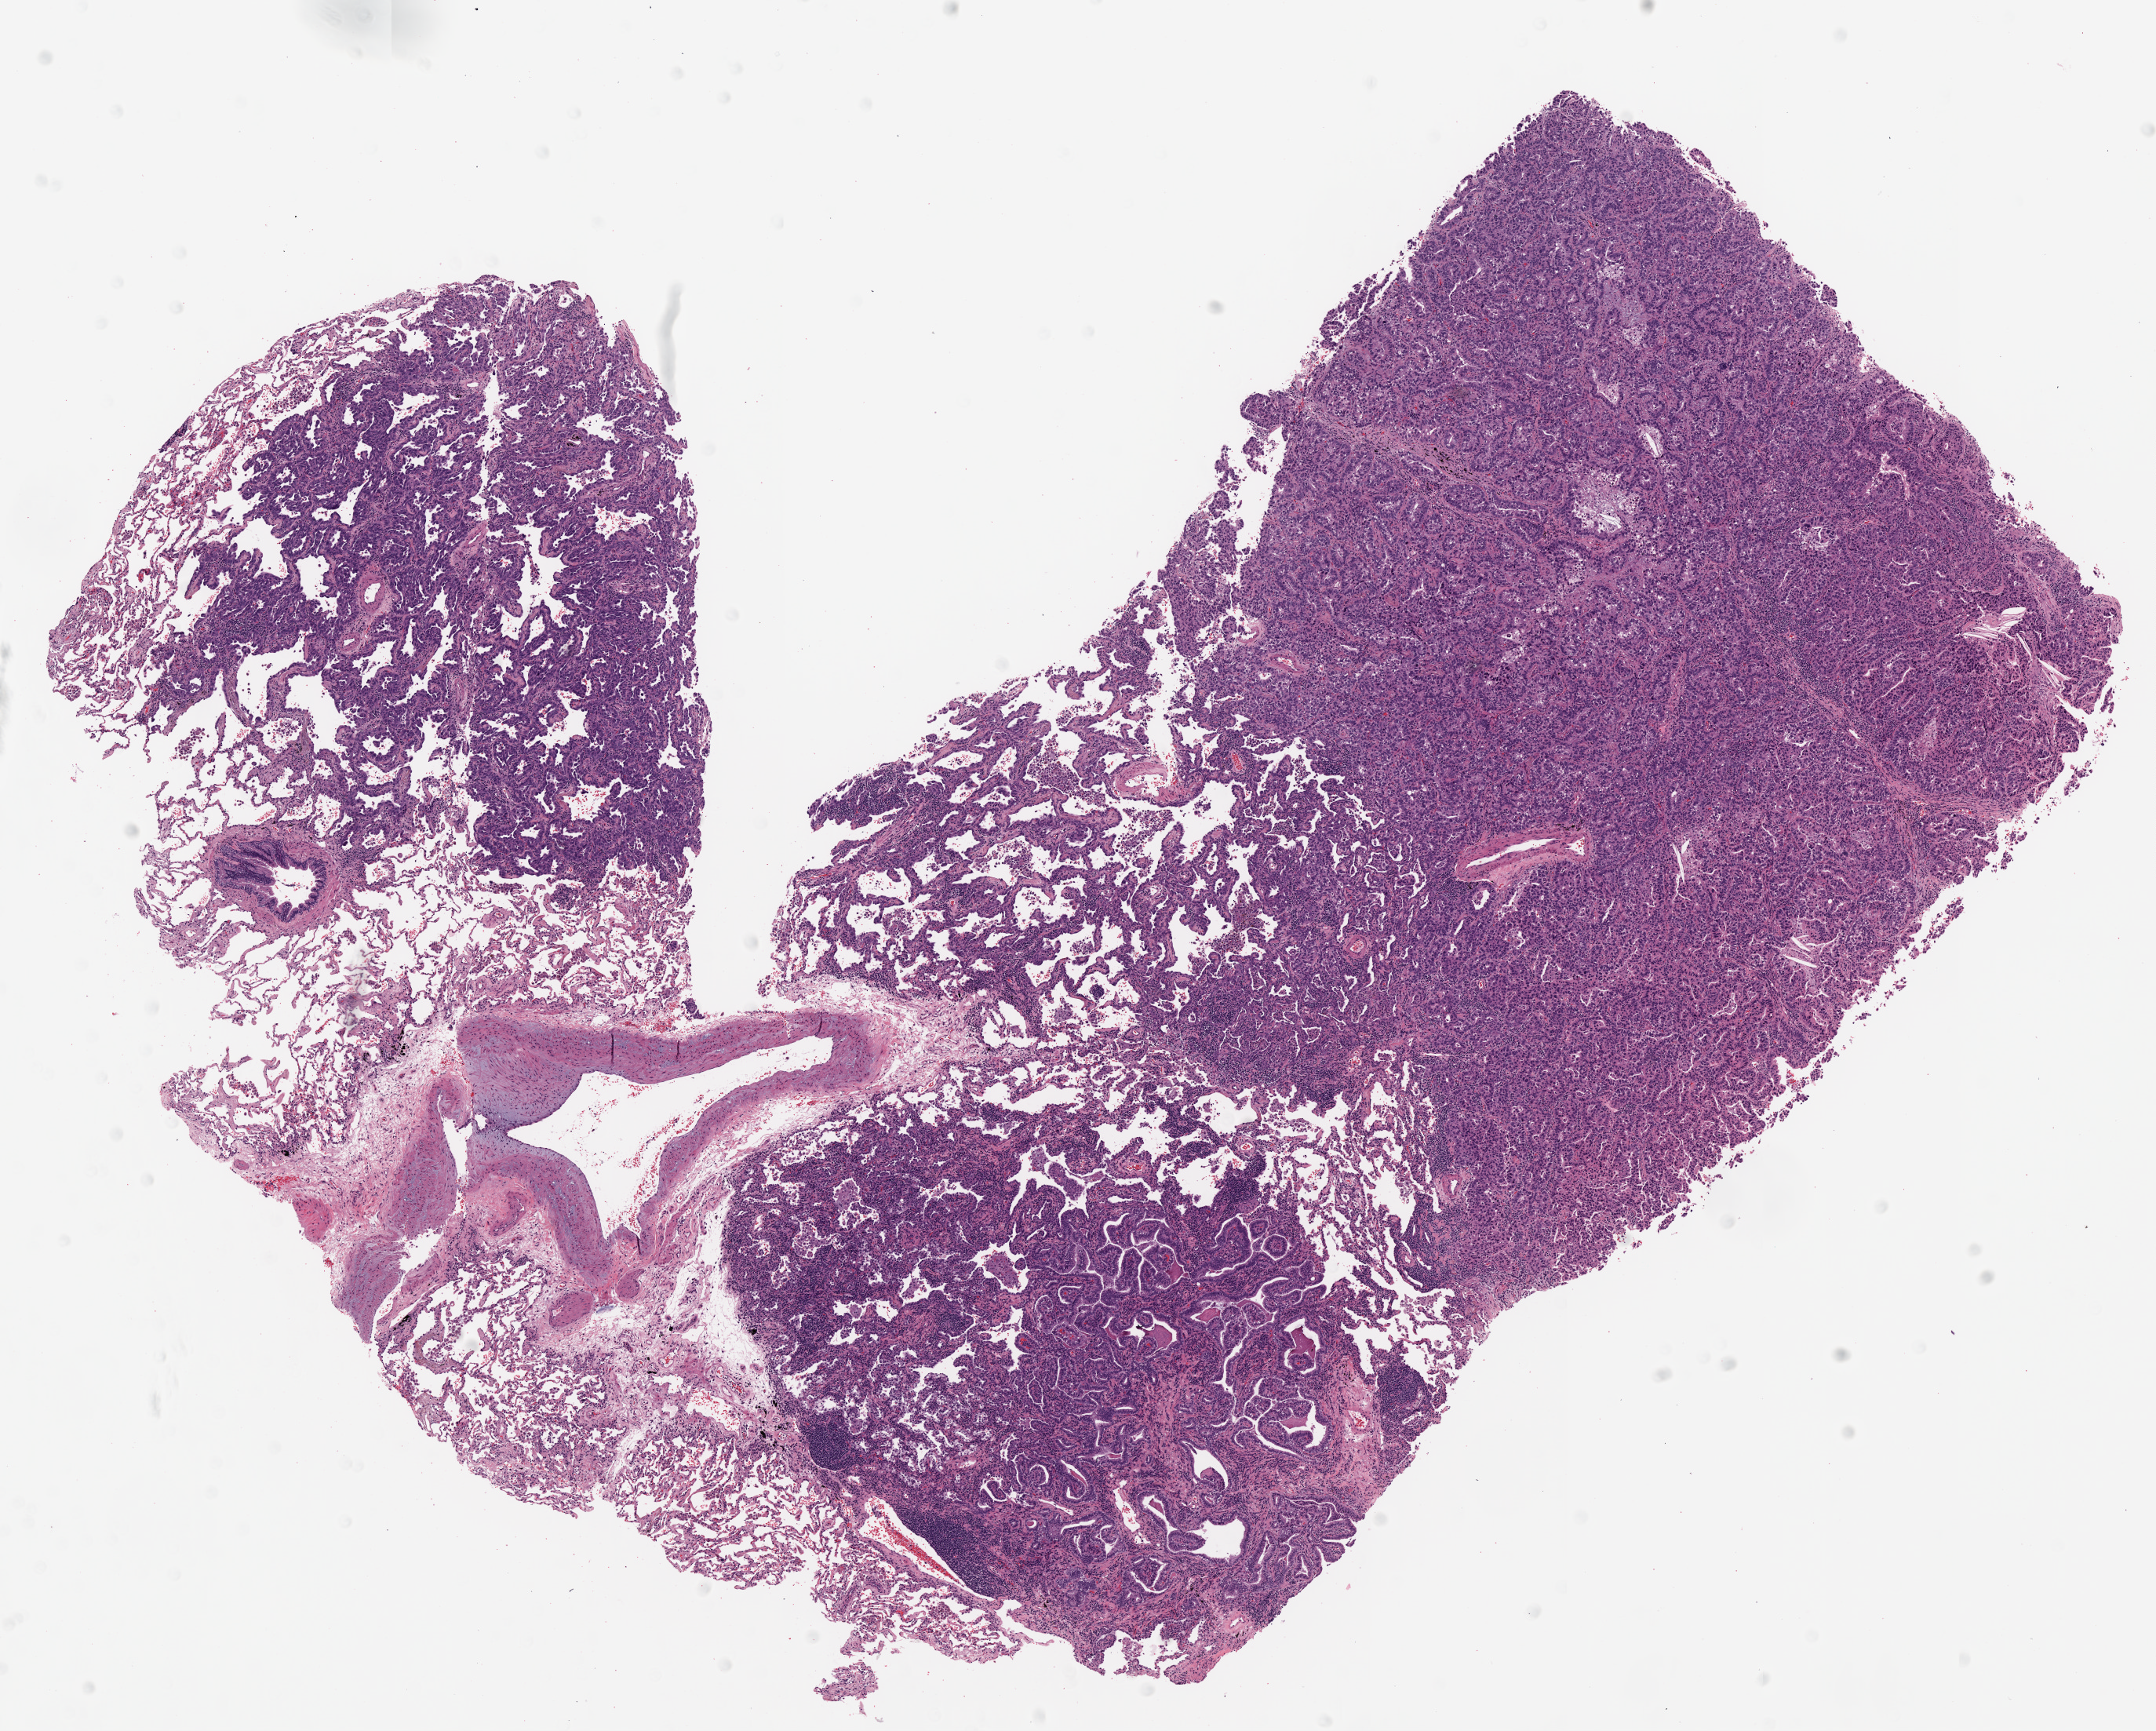
H&E-stained whole-slide image — a low-resolution overview of the entire scanned area, about 11.0 x 8.8 mm (from a 20x scan), FFPE section, primary tumour sample from the lung. Patient sex: female.
AJCC pathologic stage: IB (6th edition). Pathologic diagnosis: Adenocarcinoma, NOS.